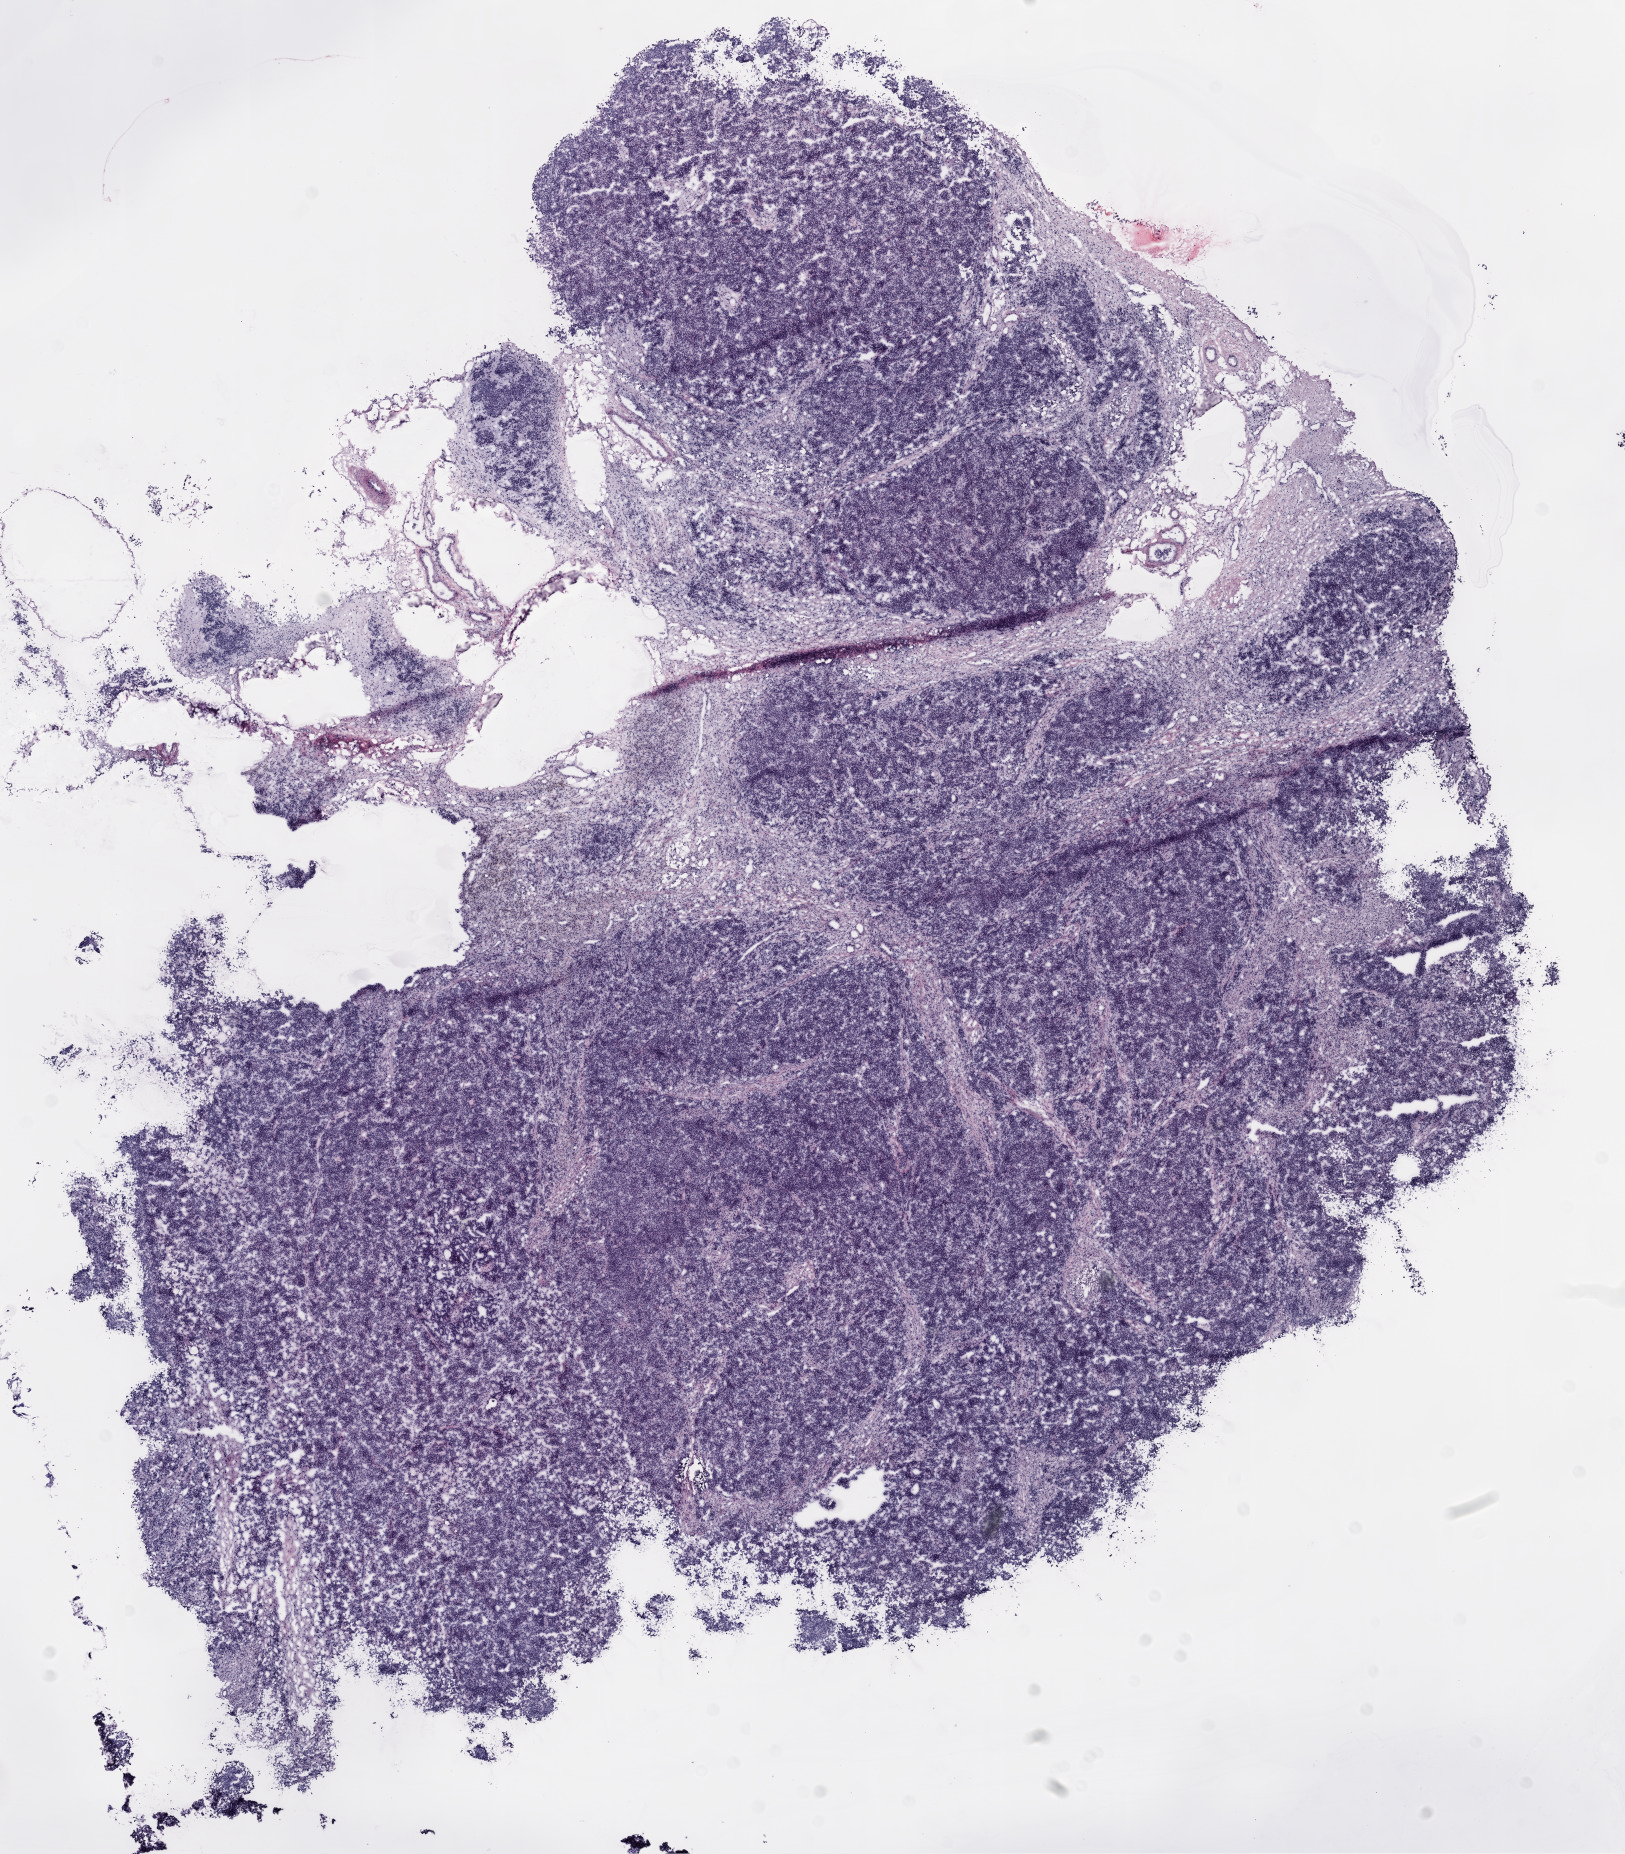
Digitized H&E tissue section (whole slide), low-resolution overview of the scanned area, about 13.0 x 14.9 mm, frozen section, ovary, recurrent tumour sample. Female, age 56 years at initial diagnosis. Composition of this section per pathologist review: tumour cells 80%, tumour nuclei 80%, normal cells 0%, stromal cells 10%, necrosis 0%.
* this section: recurrent tumour
* patient diagnosis: Serous cystadenocarcinoma, NOS